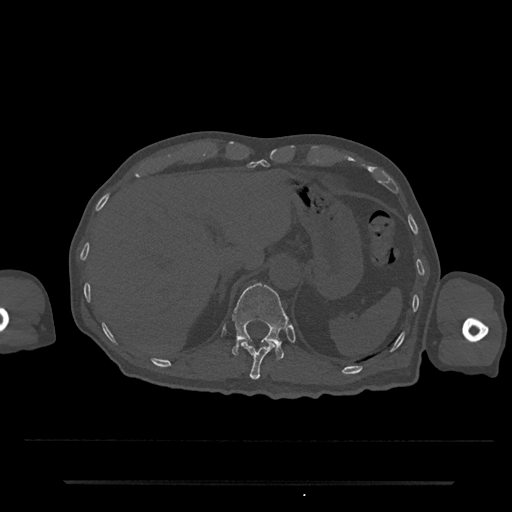
CT including the spine, one axial slice; slice 222 of 797 in the series (ordered by position); reconstruction kernel Br40s/3; 120 kVp; bone window (W 1800 / L 400 HU); 0.5 mm slice thickness; 512 × 512 image matrix, field of view 427 × 427 mm. Male patient, age 74 years. Case-level facts recorded for this patient, not image findings: primary cancer: prostate.
Structures marked on this image (semi-automatic segmentation, software-assisted and operator-edited):
- T11 vertebra: bounding box [x1, y1, x2, y2] px = [239, 340, 276, 380]
- T12 vertebra: [232, 283, 289, 359]